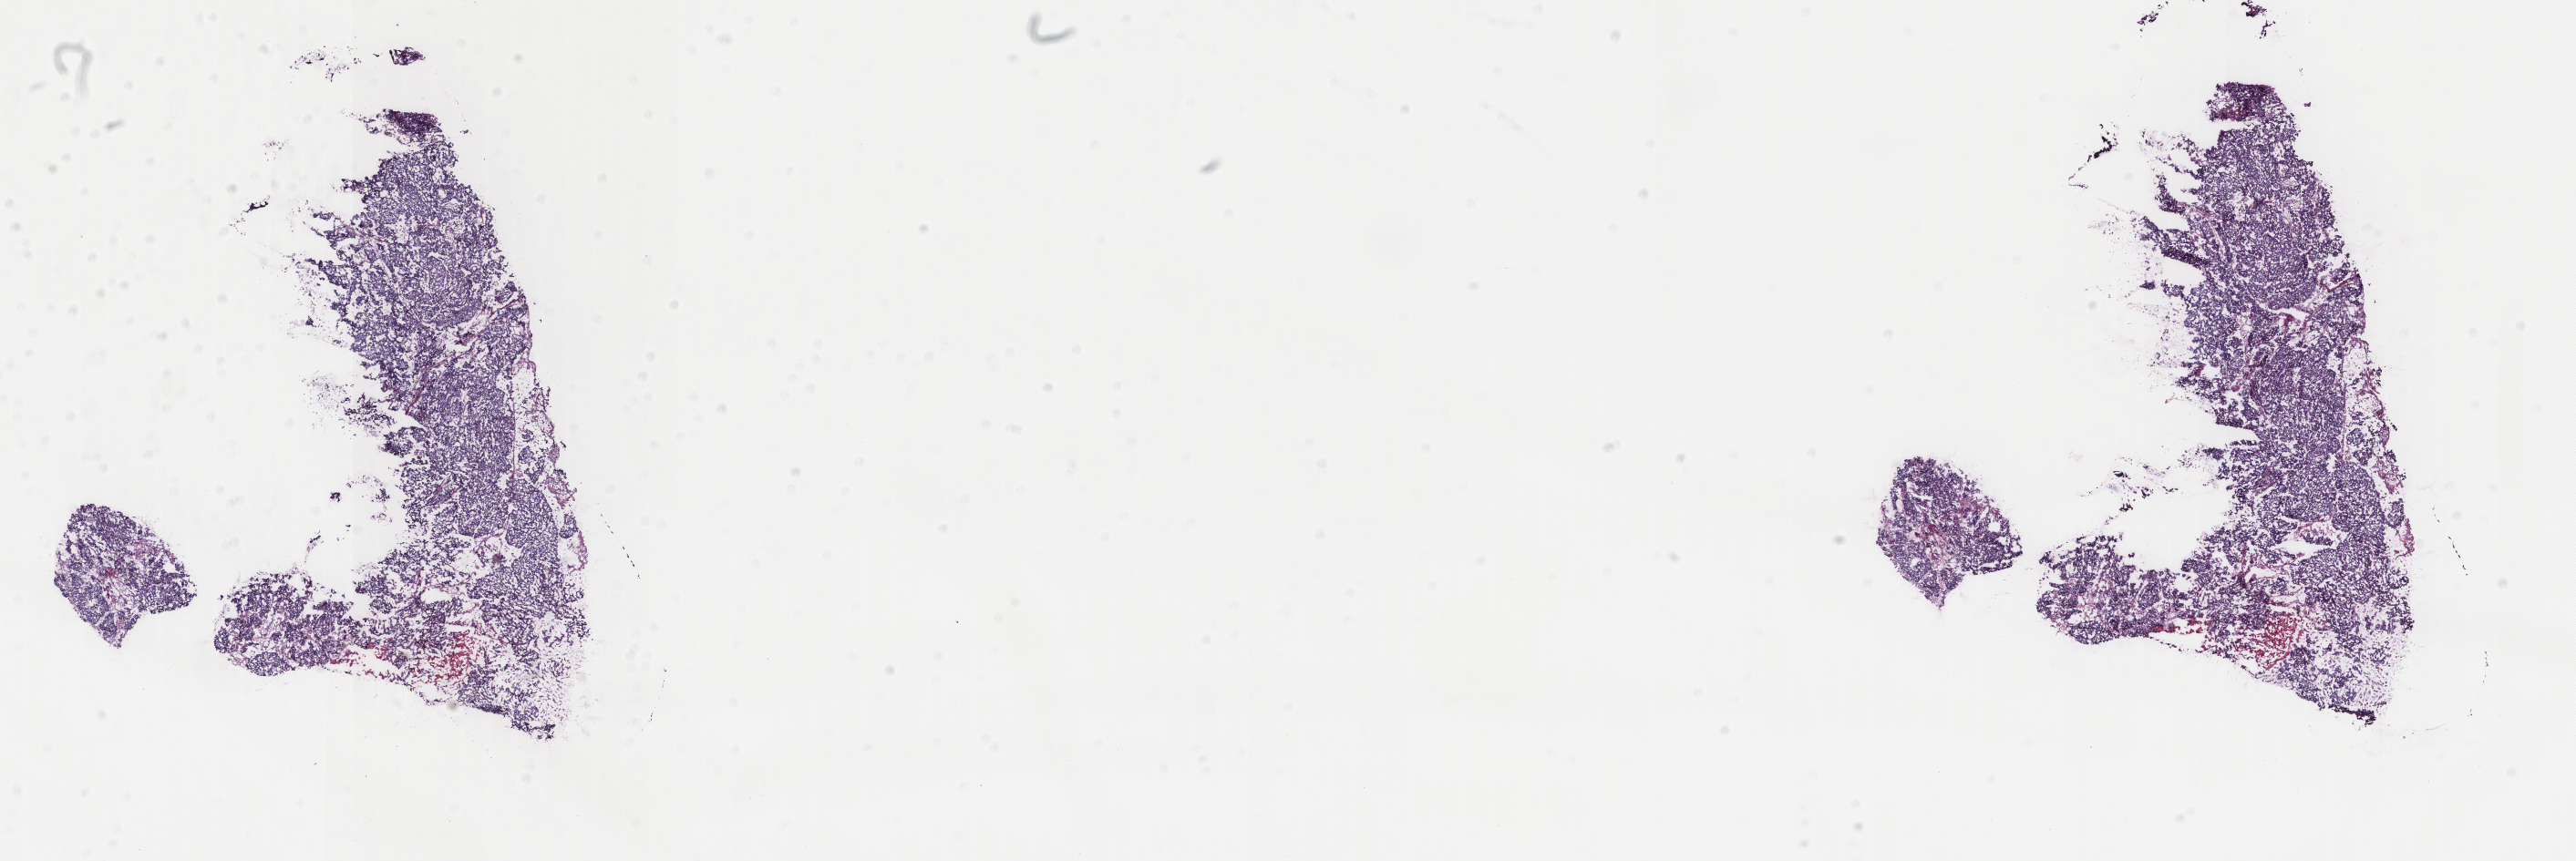
Whole-slide histology image, Hematoxylin and eosin (H&E) stained, low-resolution overview of the scanned area, about 22.4 x 7.5 mm (acquisition: 40x scan); frozen section from the top of the tissue portion; sample: primary tumour, uterus. Female, age 62 years at initial diagnosis. Histologic grade: G3 (poorly differentiated). Composition of this section per pathologist review: tumour cells 90%, tumour nuclei 97%, normal cells 0%, stromal cells 5%, necrosis 5%. Inflammatory infiltration, as recorded: lymphocyte infiltration 0%, monocyte infiltration 0%, neutrophil infiltration 0%.
FIGO stage: IIIA. Pathologic diagnosis: Endometrioid adenocarcinoma, NOS (endometrium).